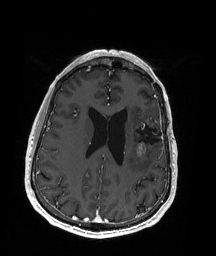
Brain MRI from a brain-tumour surgery series, one axial slice; slice 73 of 192 in the series (ordered by position); T1-weighted post-contrast; 1 mm slice thickness; 216 × 256 image matrix, field of view 211 × 250 mm. Case-level facts recorded for this patient, not image findings: histopathology: Oligodendroglioma; WHO grade: 2; IDH mutation: yes; tumour location: Left Insular.
Outlined on this slice (manually delineated by an expert):
- previous resection cavity: box from (x=132, y=121) to (x=163, y=148) px
- tumour: (x=137, y=118)–(x=154, y=157)